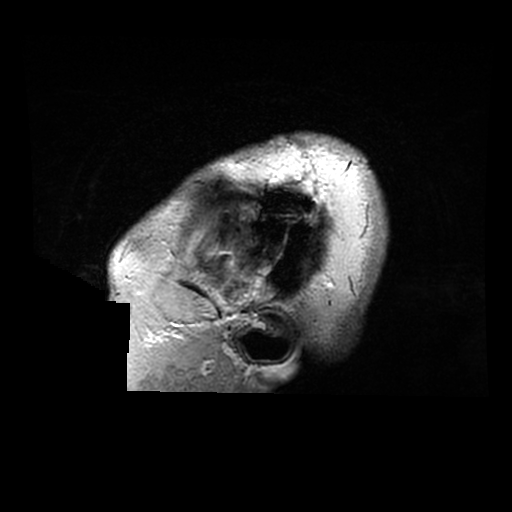
Brain MRI from a brain-tumour surgery series, one sagittal slice. Position 268 of 320 along the scan axis. 0.6 mm slice thickness. 512 × 512 image matrix. Case-level facts recorded for this patient, not image findings: histopathology: Astrocytoma; WHO grade: 2; IDH mutation: yes.
Annotated regions visible in this slice (manually delineated by an expert):
- tumour: bounding box <274,248,281,257> (left, top, right, bottom; pixels)